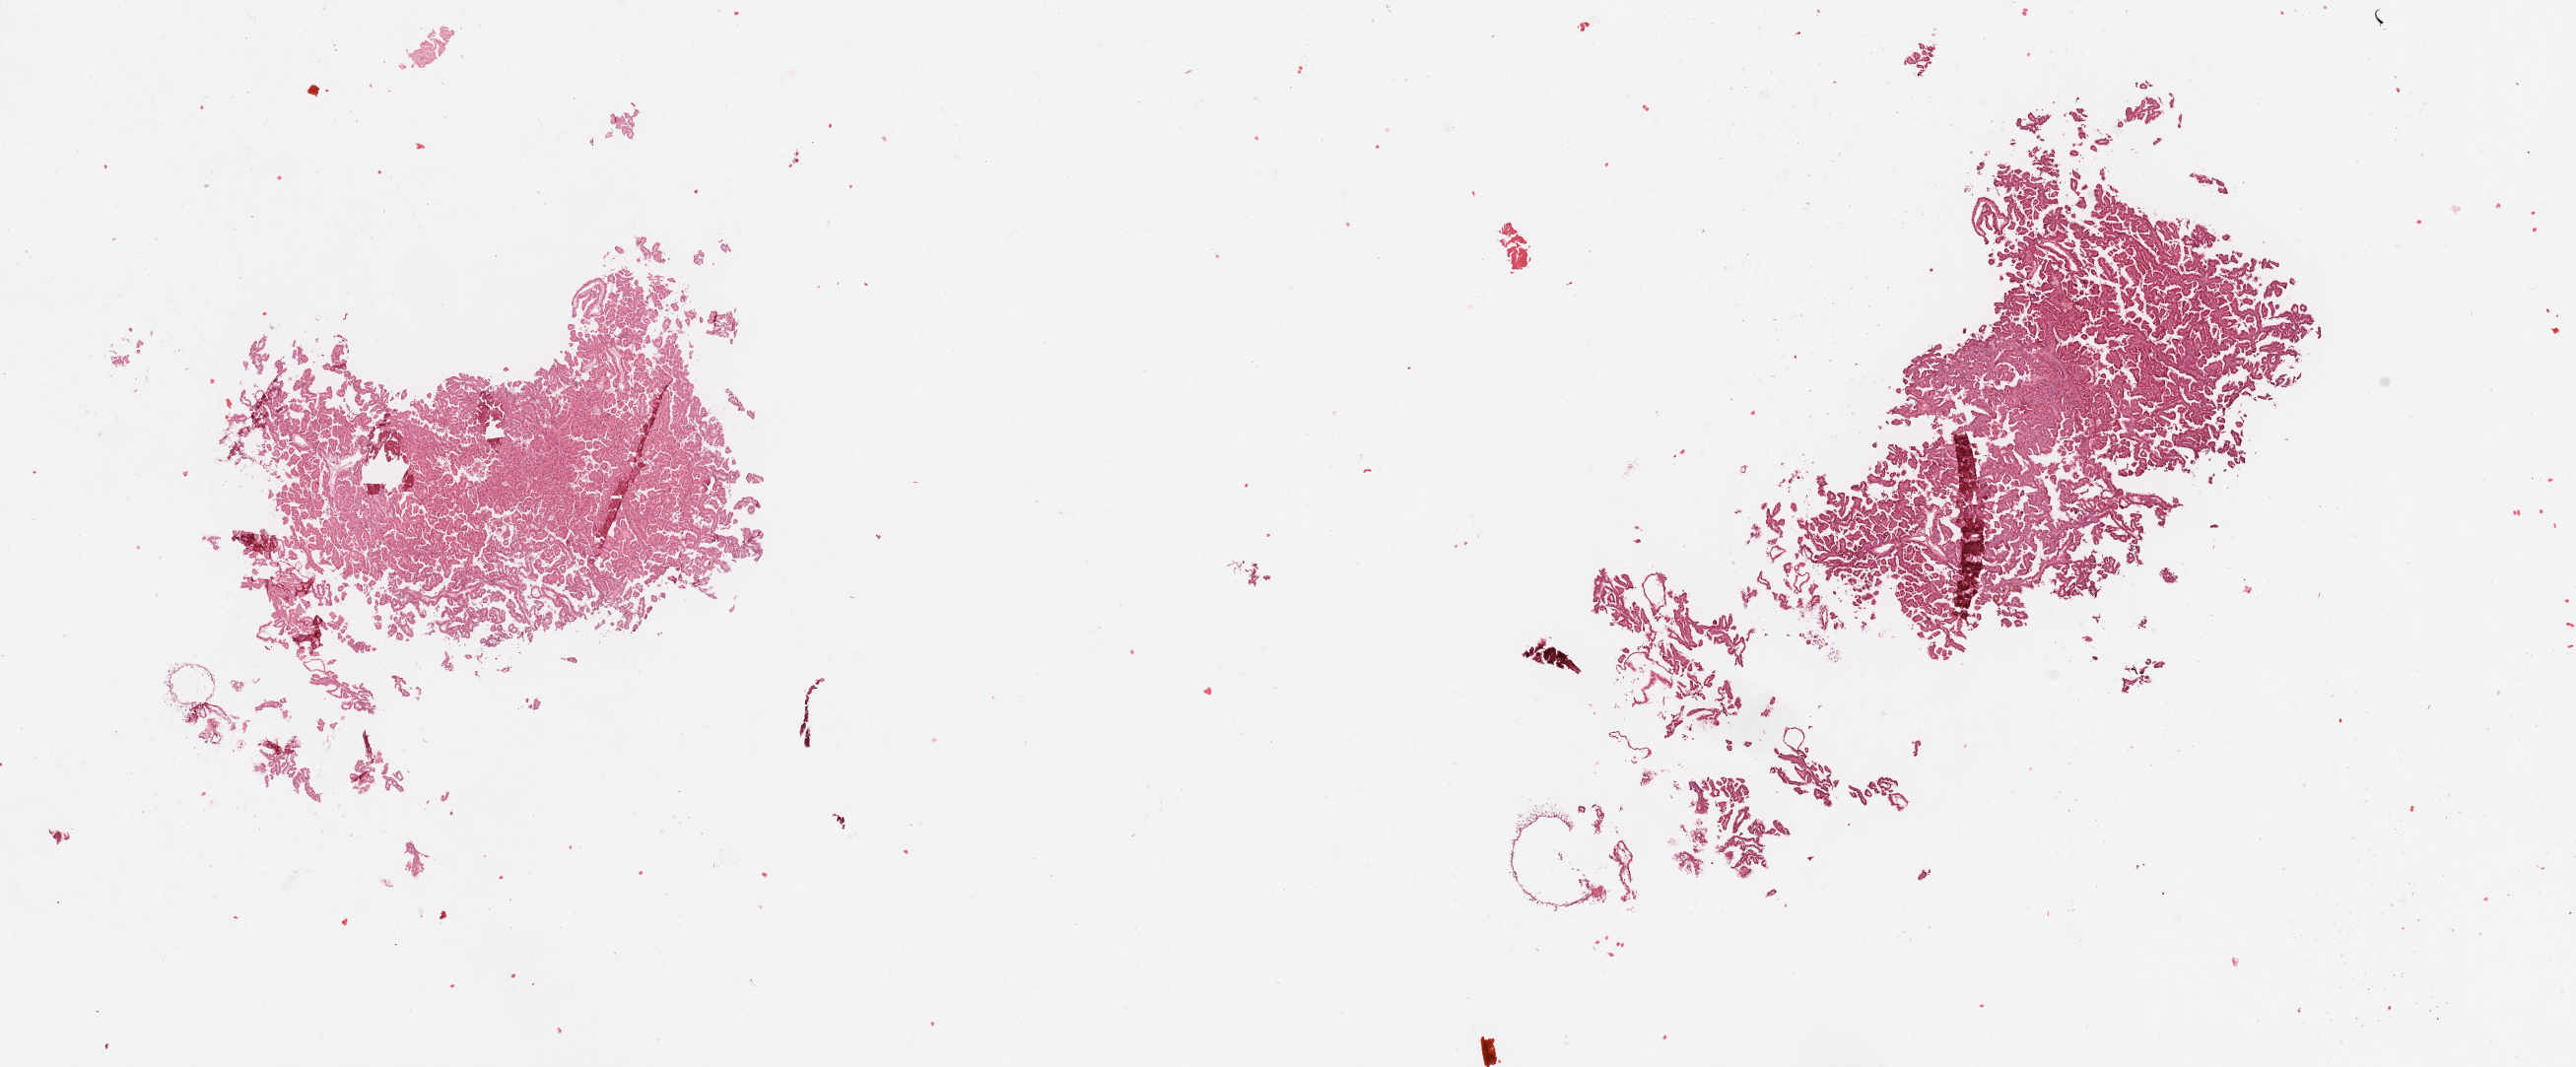
Whole-slide histology image, H&E — a low-resolution overview of the entire scanned area, about 20.7 x 8.6 mm (from a 20x scan). Tumour tissue sample, sampled site: kidney. 79-year-old male patient. Histologic grade: G2 (moderately differentiated). Pathologist review of this section (percent, as recorded): tumour nuclei 90%, necrosis 0%.
- histologic diagnosis: Renal cell carcinoma, NOS
- AJCC pathologic stage: I
- primary tumour site (as recorded): lower pole